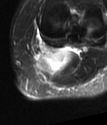
MRI of an extremity soft-tissue mass, one axial slice. Position 51 of 78 along the scan axis. T2-weighted fat-saturated. MR volume resampled by the dataset authors to the PET/CT grid (not the native acquisition matrix). 107 × 125 image matrix, field of view 104 × 122 mm. Female patient. From the clinical record (not read from this slice): histological type: extraskeletal high grade osteogenic sarcoma; grade: high; site of the primary tumour: left calf.
Annotated regions visible in this slice (expert contour drawn on MRI and transferred to this co-registered scan by the dataset authors):
- gross tumour volume (mass): bounding box (x1, y1, x2, y2) in pixels: (37, 49, 70, 76)